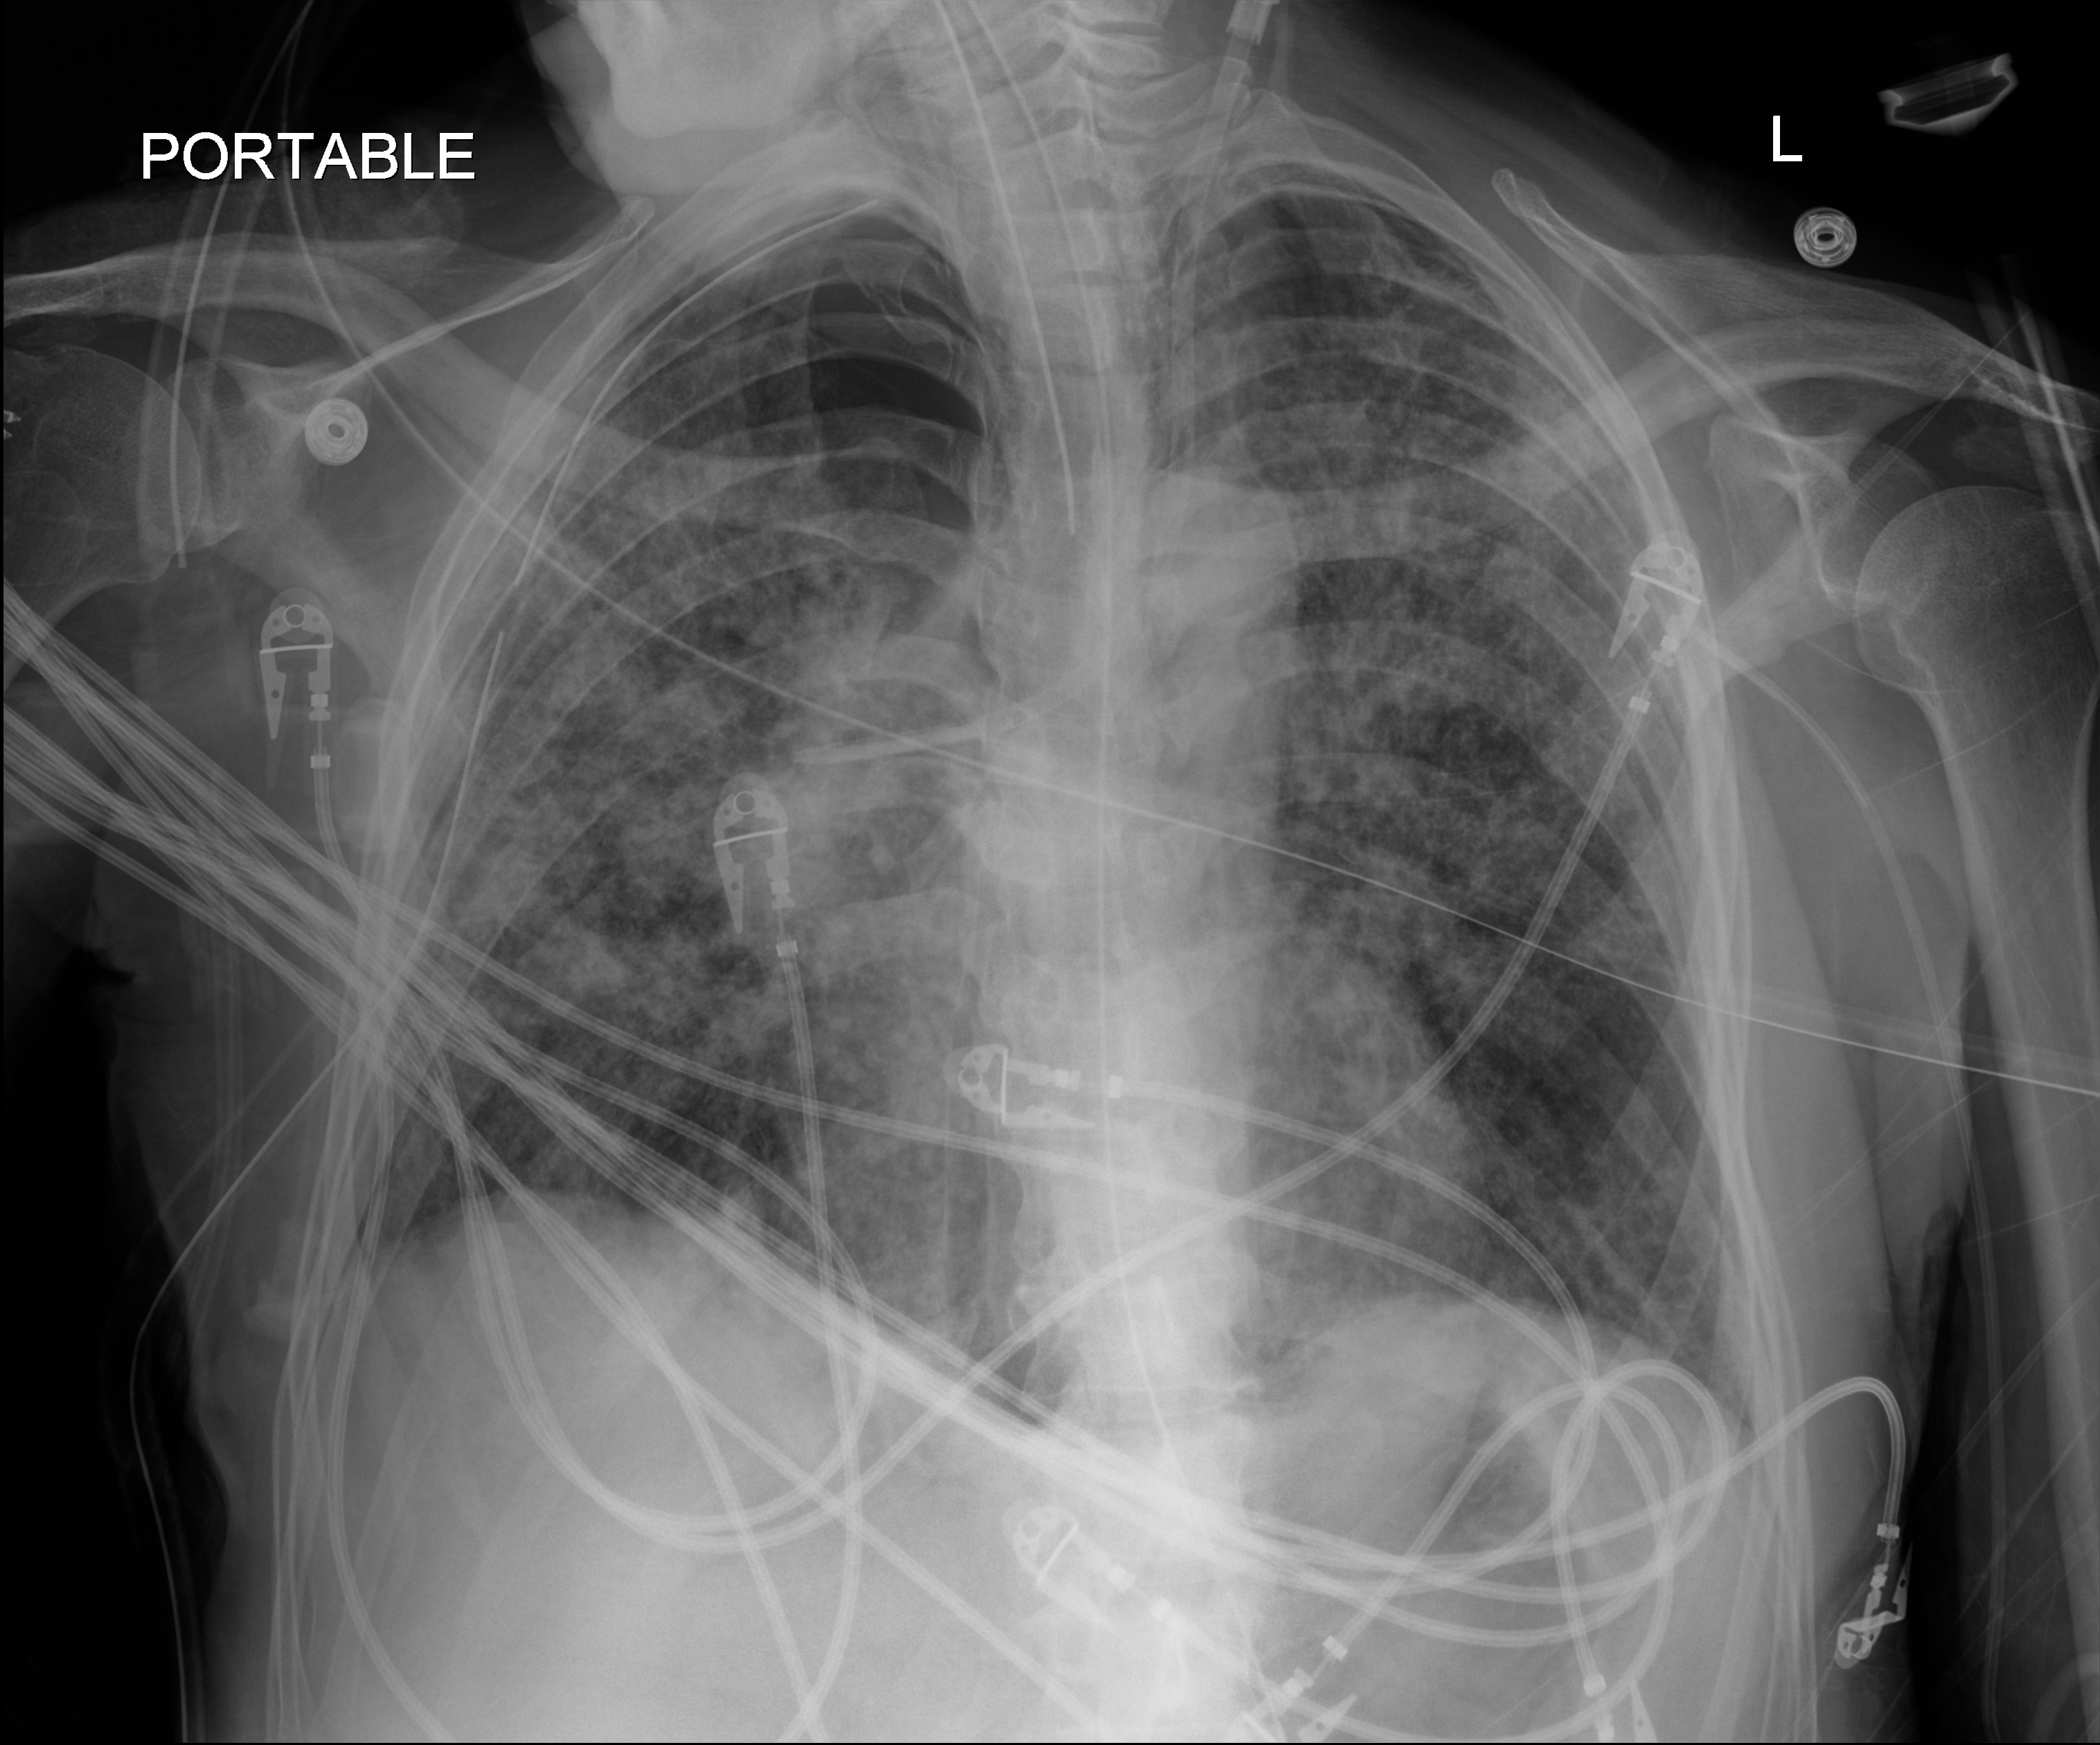
Portable chest radiograph, anteroposterior (AP) projection. Male patient hospitalised with COVID-19, age 60–74 years.
Hospital-stay facts (about this admission, not read from this image; timing relative to this image not recorded):
- length of hospital stay: 65 days
- mechanically ventilated during this hospital stay: yes